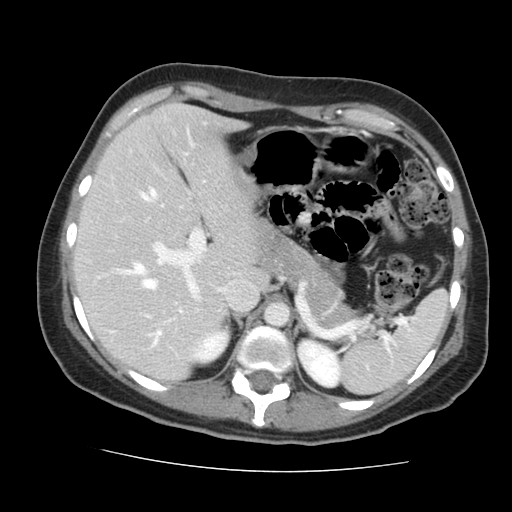
Contrast-enhanced abdominal CT, one axial slice. Position 99 of 144 along the scan axis. 120 kVp. Intravenous contrast given. Soft-tissue window (W 400 / L 40 HU). 2.5 mm slice thickness. 512 × 512 image matrix, field of view 333 × 333 mm. Female patient, age 46 years. From the clinical record (not read from this slice): diagnosis: colorectal cancer liver metastases, imaged before liver resection; multiple liver metastases: no; largest metastasis: 2.8 cm.
Structures marked on this image (manually delineated by an expert):
- hepatic veins: bounding box (x1, y1, x2, y2) in pixels: (141, 190, 163, 289)
- liver: (77, 105, 266, 379)
- planned liver remnant (the part of the liver to remain after resection): (77, 105, 266, 379)
- portal vein (with intrahepatic branches): (120, 228, 206, 345)